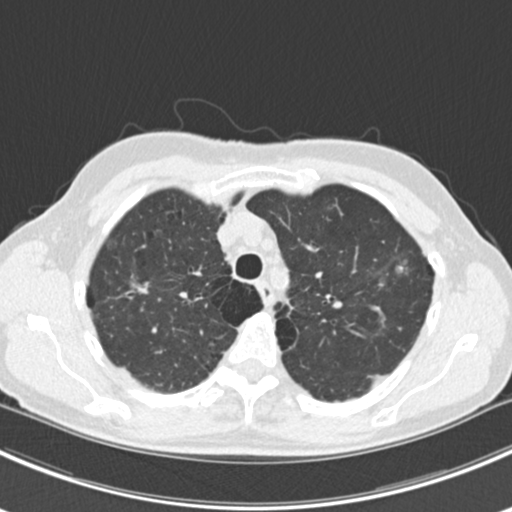
Chest CT (low-dose screening protocol), one axial image, first (baseline) screen, lung window (W 1500 / L -600 HU), 2 mm slice thickness, standard (soft-tissue) reconstruction kernel (B30f), slice 45 of 224 in the series. Female participant, aged 63 years at enrolment. Current smoker at enrolment.
Expert-annotated lung lesion, box from (x=364, y=238) to (x=435, y=309) px. The screening reader recorded 10 non-calcified nodules or masses ≥4 mm on this exam (right lower lobe, right lower lobe, left lower lobe, left lower lobe, right middle lobe, right lower lobe, left lower lobe, left upper lobe, right upper lobe, left upper lobe); which of them this box marks is not recorded. Official screen result: positive, change unspecified: nodule(s) >= 4 mm or enlarging nodule(s), mass(es), or other non-specific abnormalities suspicious for lung cancer. Lung cancer was diagnosed 751 days after this screen (after the third annual screen): bronchiolo-alveolar adenocarcinoma, NOS, right upper lobe, right middle lobe, right lower lobe, left upper lobe, left lower lobe, moderately differentiated (G2), stage IV (AJCC 6th edition).